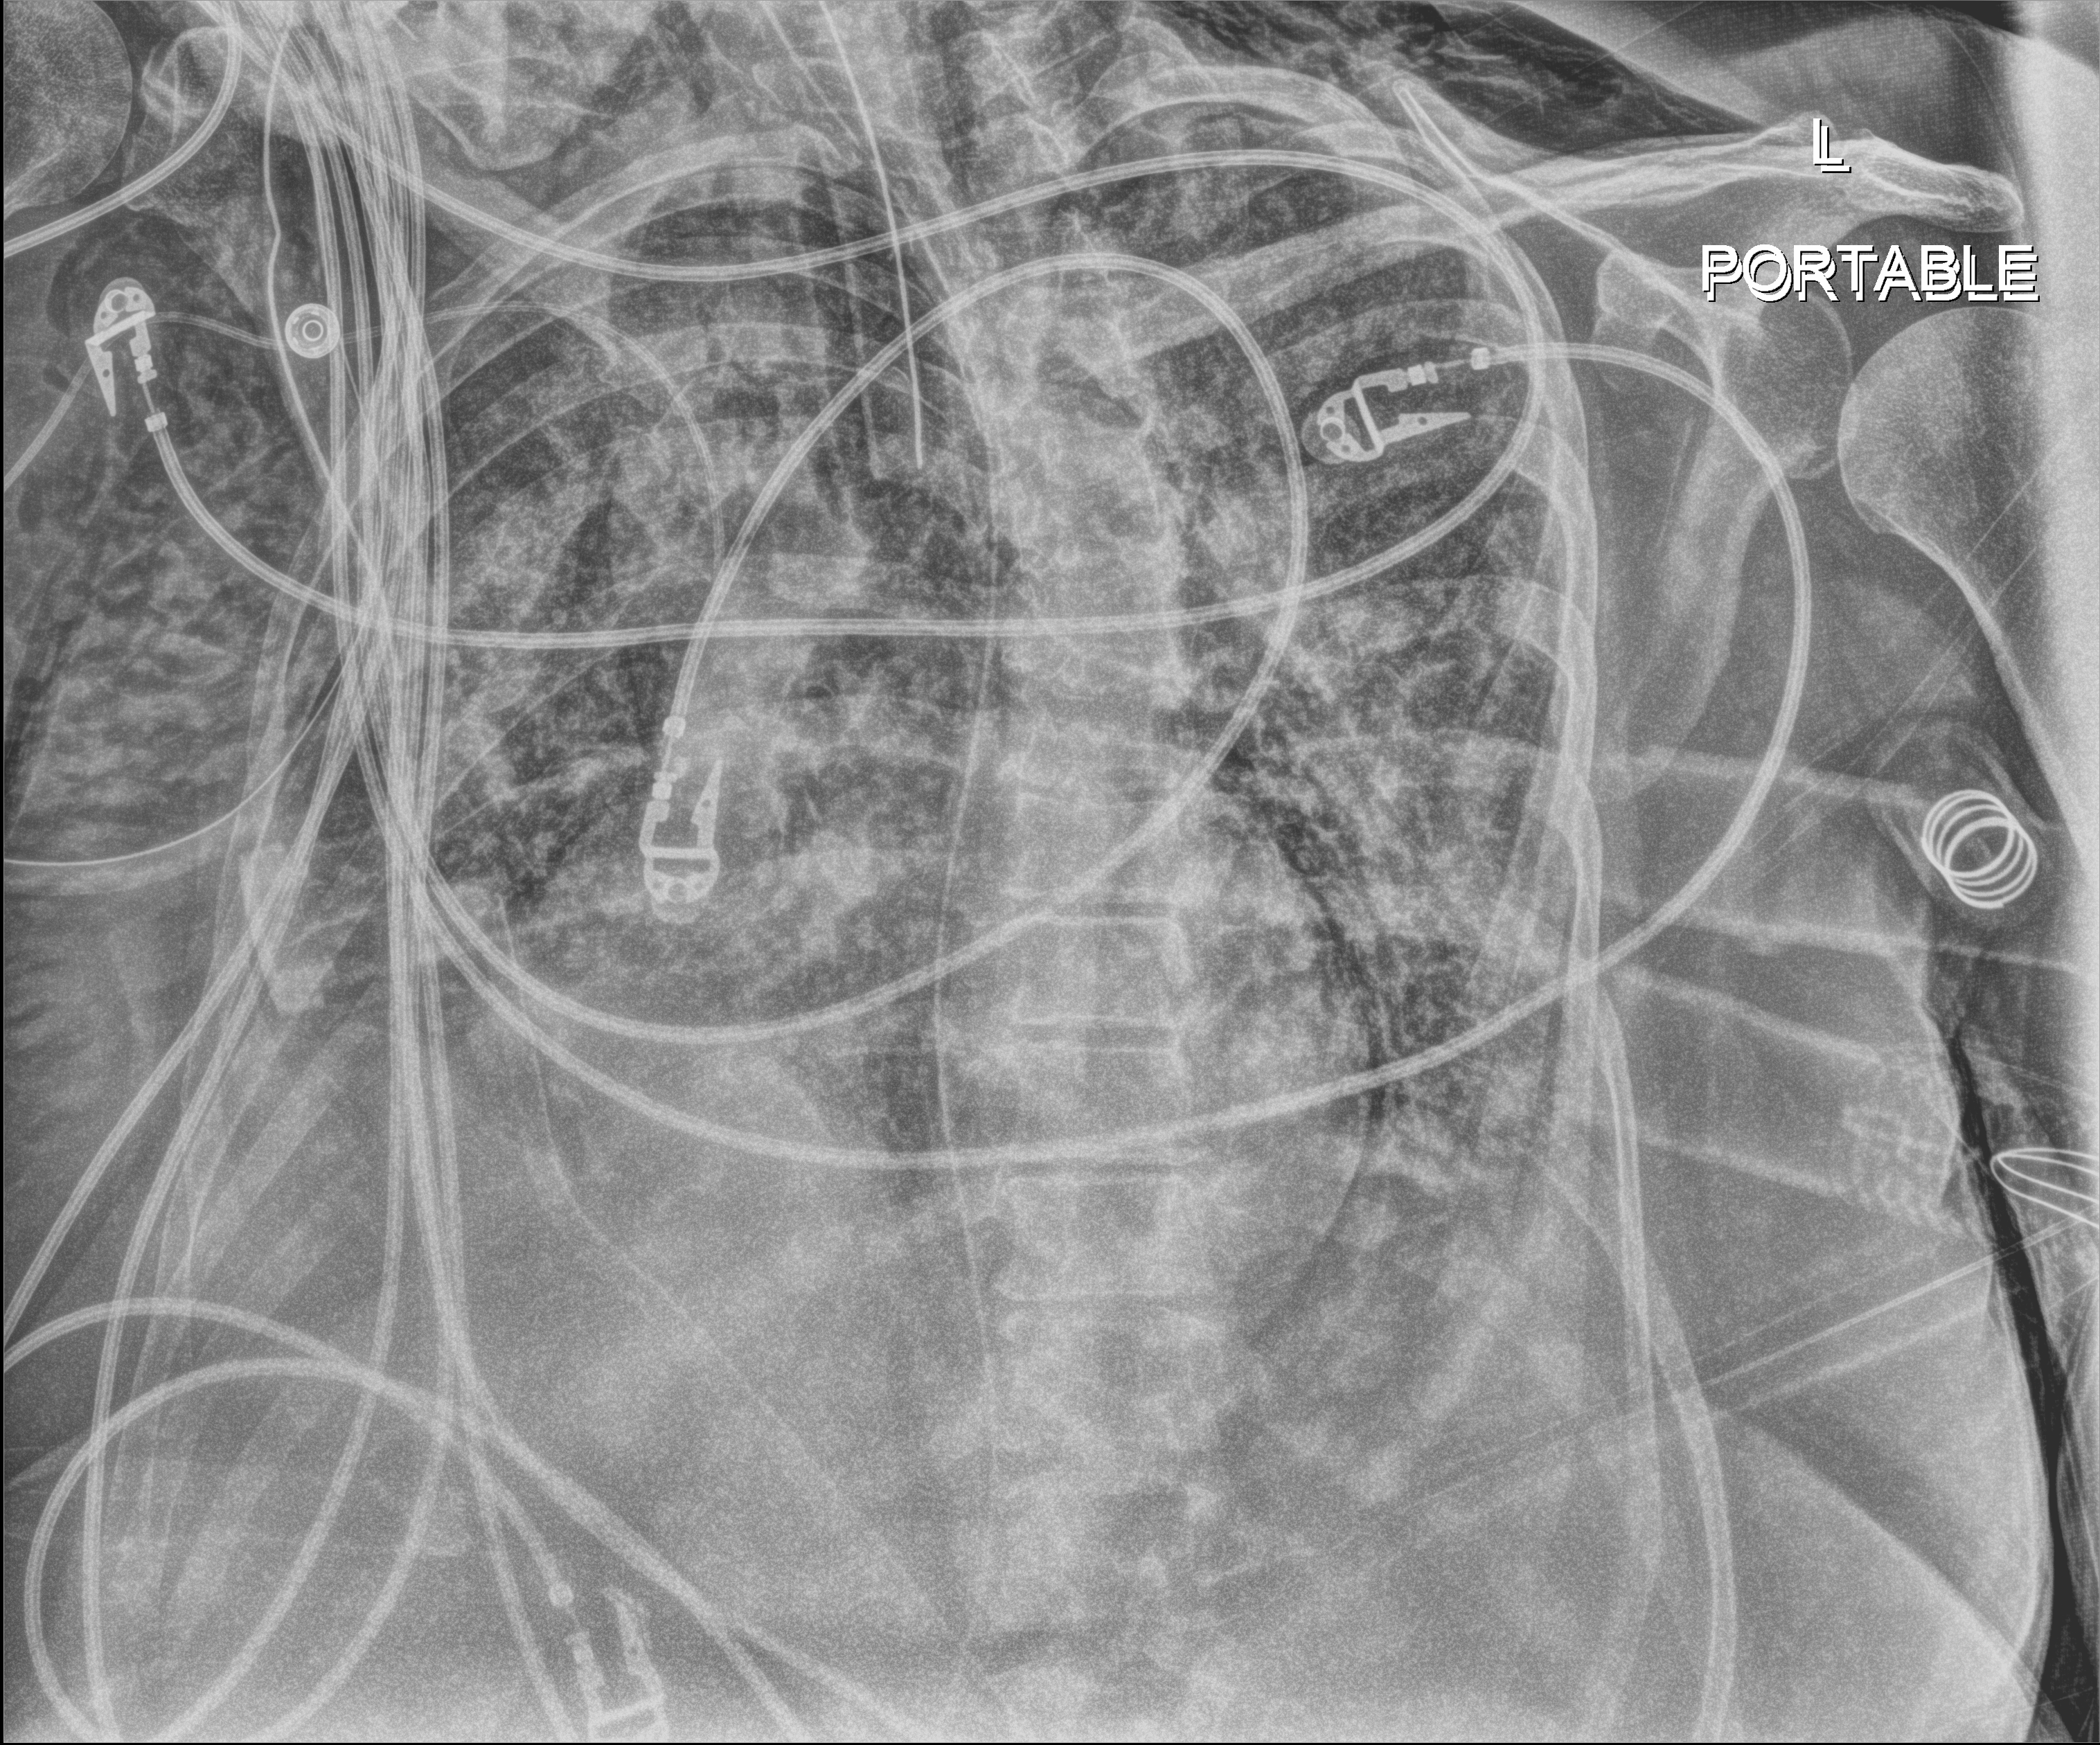
Portable chest radiograph. Female patient hospitalised with COVID-19, age 60–74 years.
From the hospital-stay record, not from the radiograph (when in the stay this image was taken is not recorded): mechanically ventilated during this hospital stay: yes; admitted to intensive care during this hospital stay: yes.